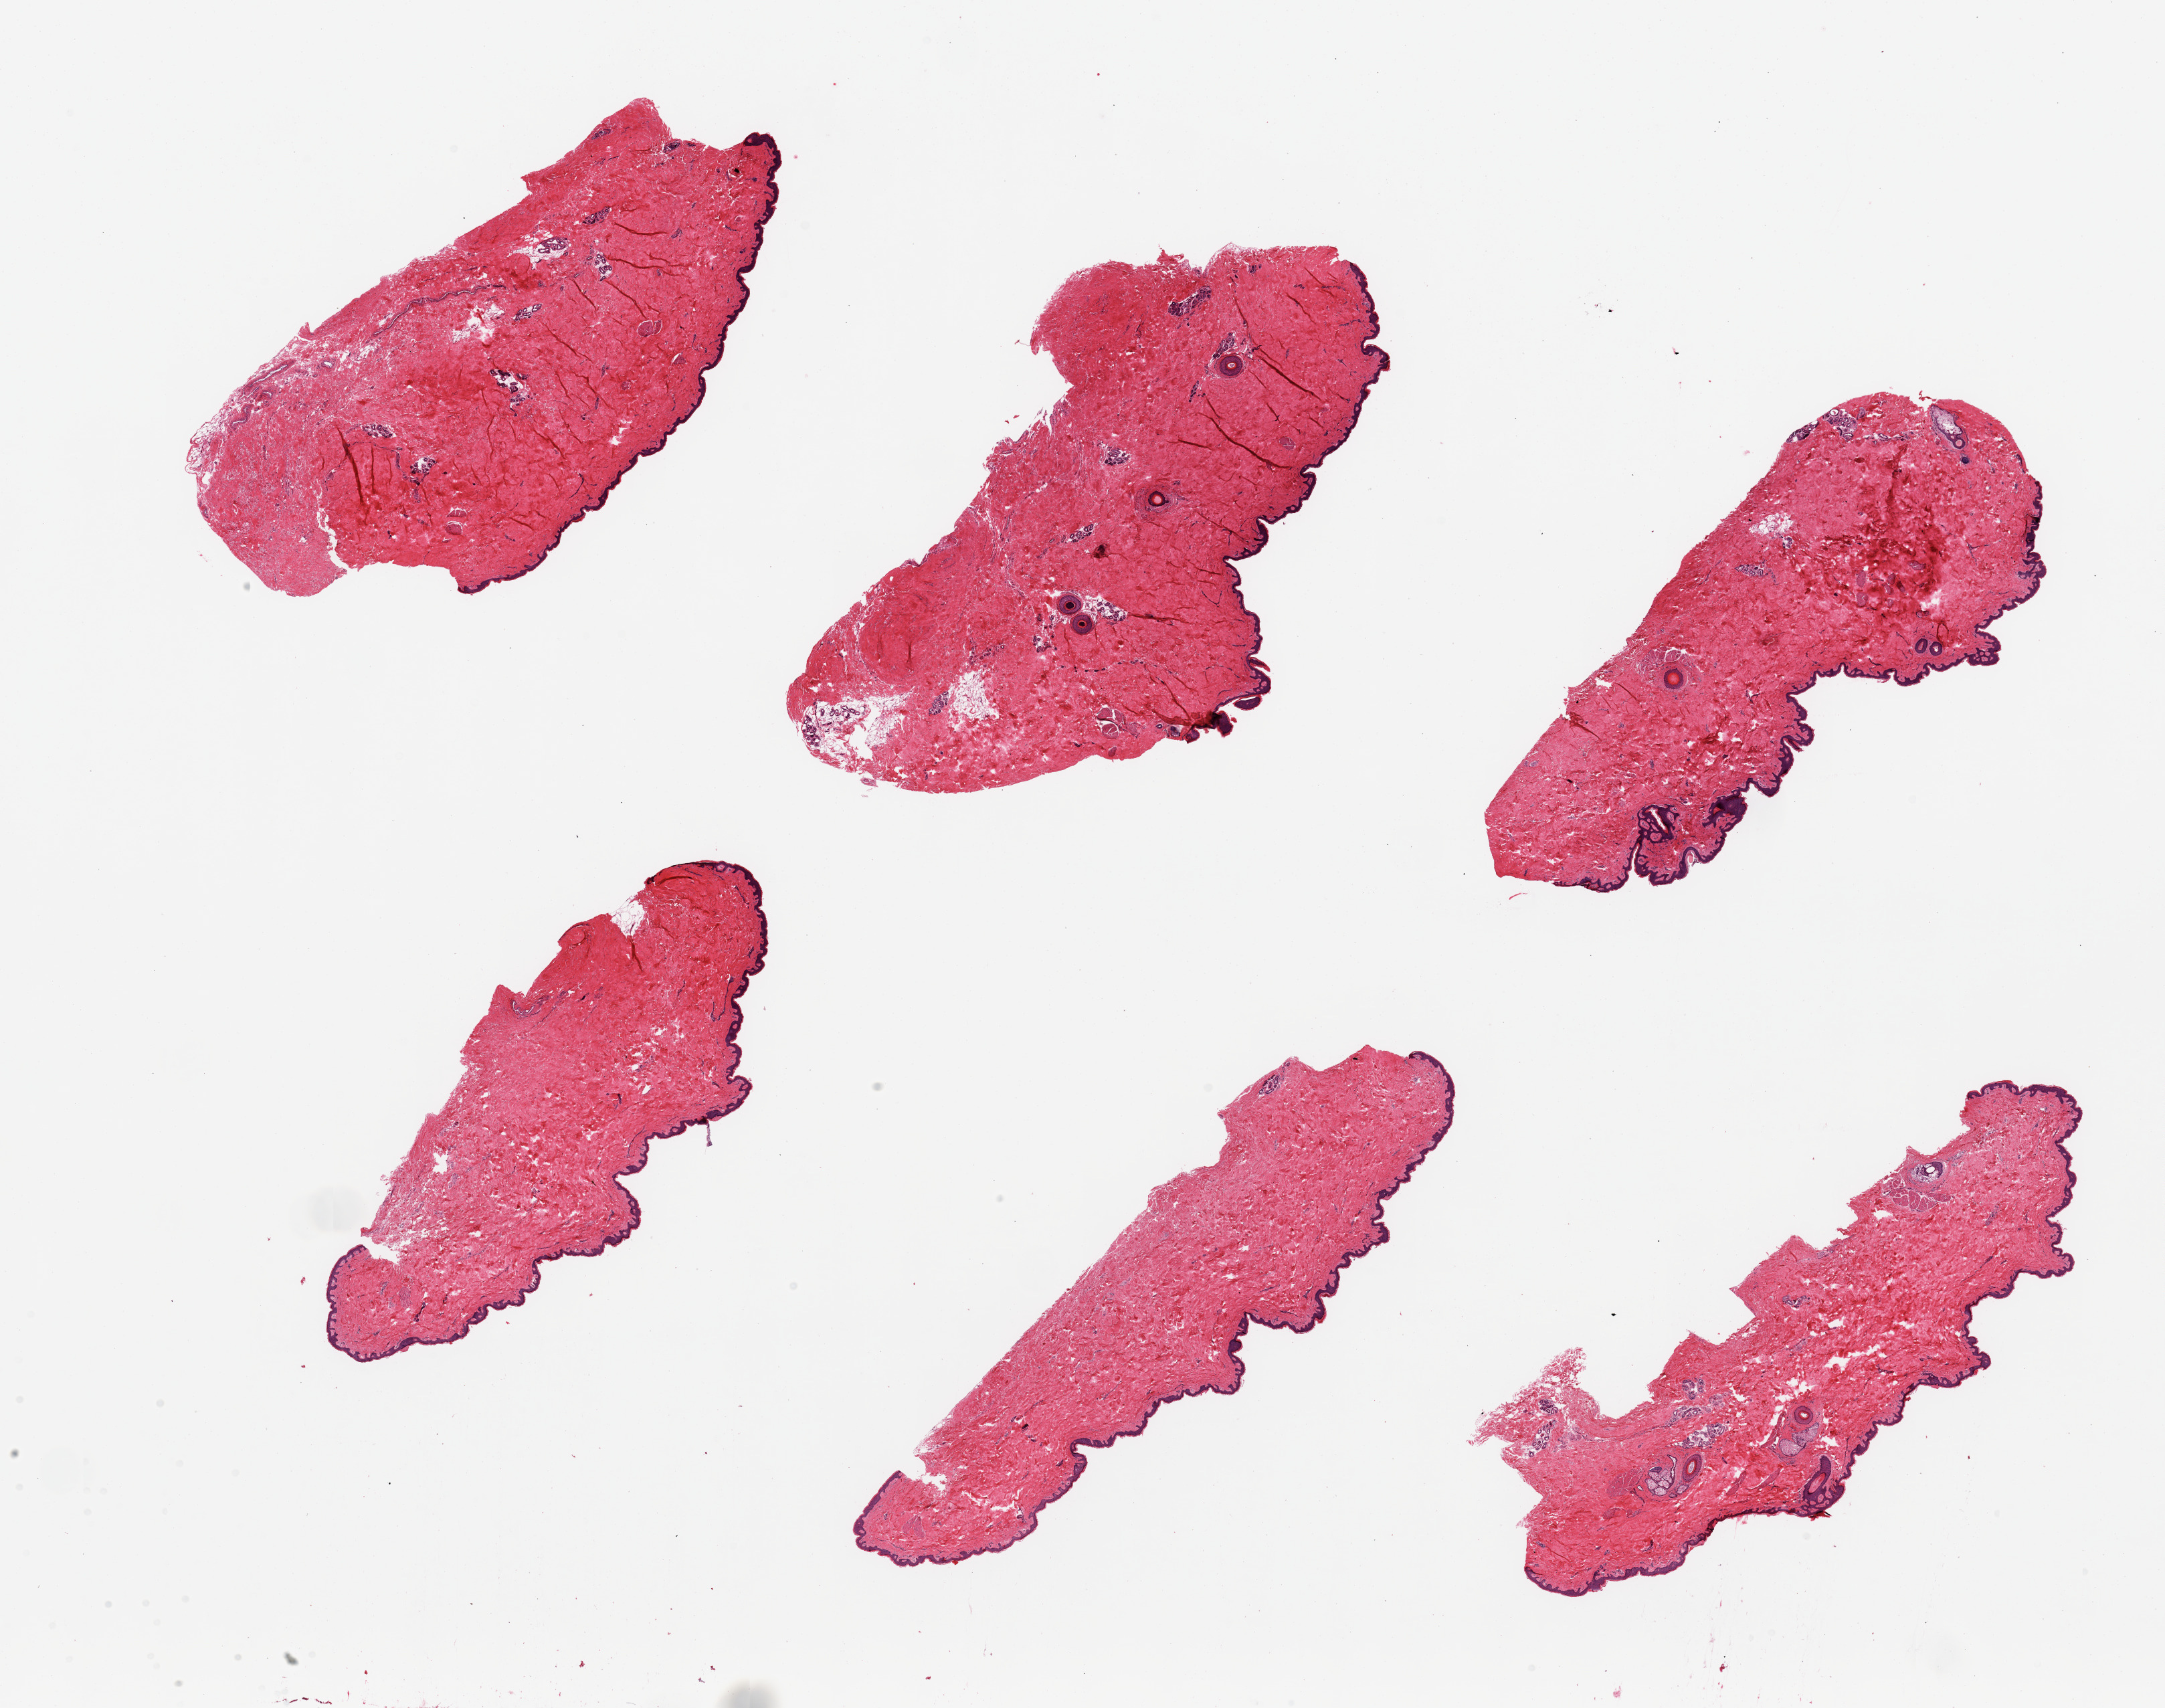
Digitized hematoxylin and eosin (H&E)-stained section, shown as a low-resolution overview of the whole scanned area (about 25.6 x 20.2 mm); PAXgene-fixed, paraffin-embedded tissue; target tissue: skin of suprapubic region; donor tissue sample. Female donor.
Pathologist's review note for this sample: 6 pieces, no adherent dermal fat, squamous epithelium is ~50 microns.